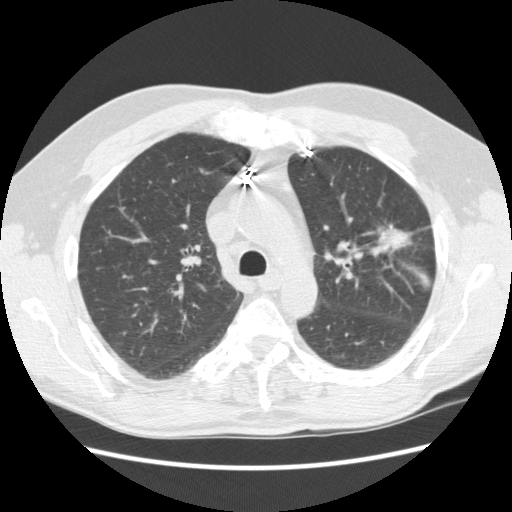
Low-dose screening chest CT, one axial slice. Reconstruction kernel STANDARD. Lung window (W 1500 / L -600 HU). 512 × 512 image matrix, field of view 362 × 362 mm.
Outlined on this slice (expert manual segmentation):
- lesion 1 (tumor, upper lobe of left lung): bounding box [x1, y1, x2, y2] px = [378, 225, 411, 251]